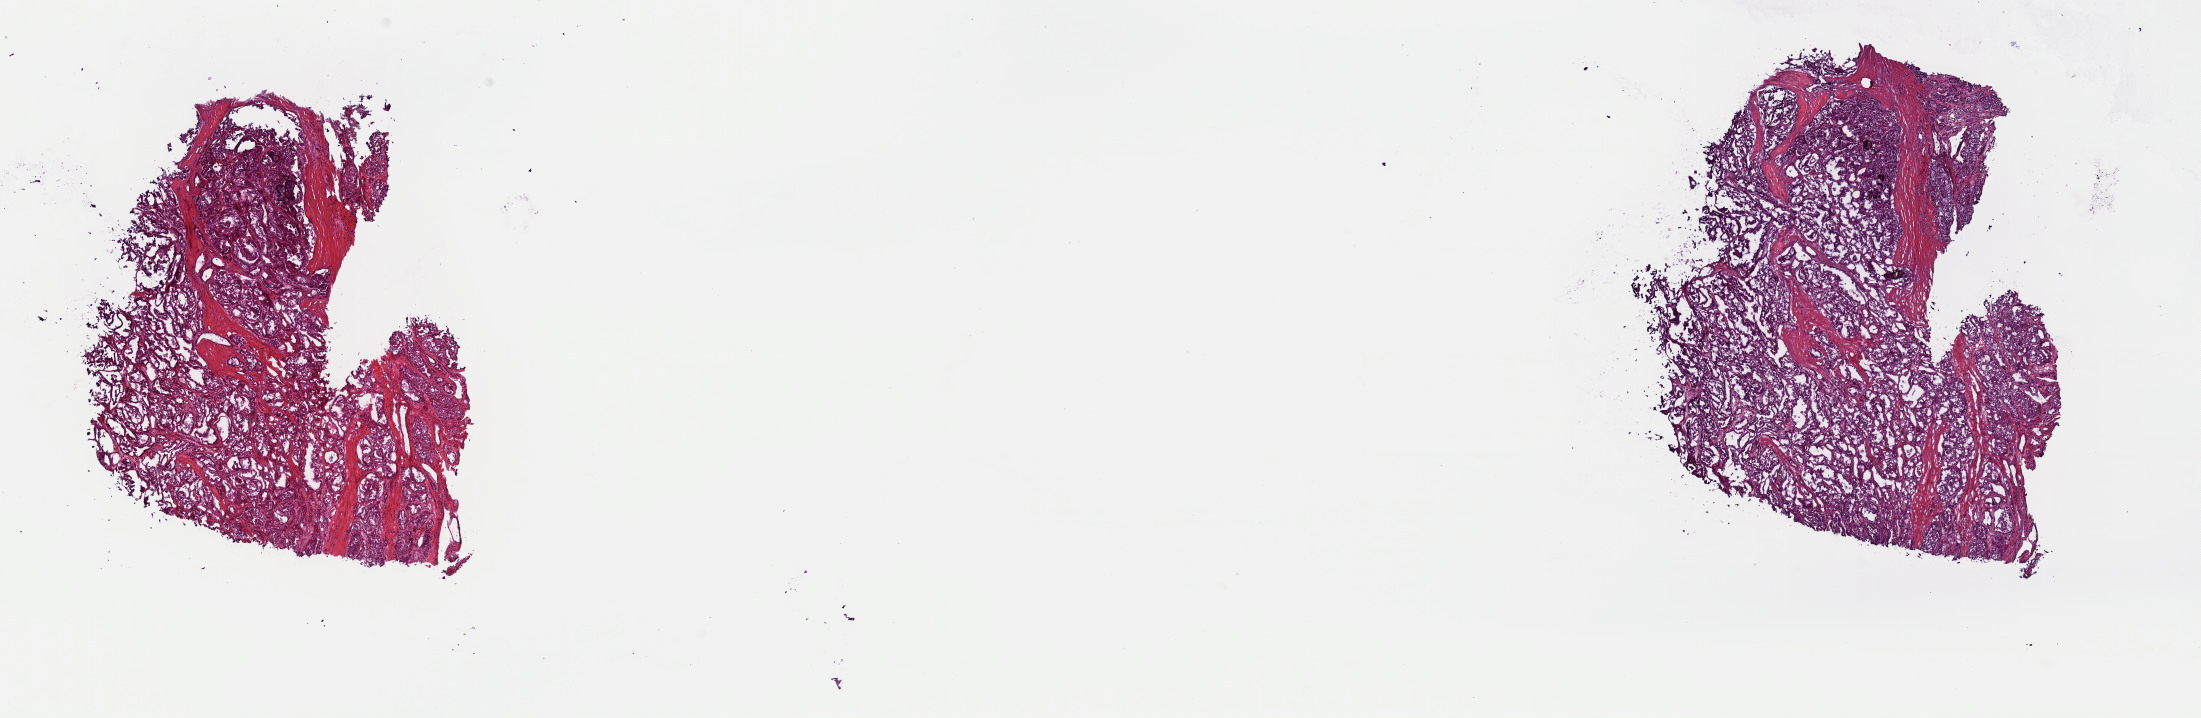
Digitized H&E-stained tissue section (whole slide) — a low-resolution overview of the entire scanned area, about 17.4 x 5.7 mm (from a 40x scan), frozen section, primary tumour sample from the thyroid. Male, age 63 years at initial diagnosis. Composition of this section per pathologist review: tumour cells 100%, tumour nuclei 88%, normal cells 0%, stromal cells 0%, necrosis 0%. Infiltration values recorded for this section: lymphocyte infiltration 0%, monocyte infiltration 0%, neutrophil infiltration 0%.
• histologic diagnosis: Papillary adenocarcinoma, NOS (thyroid gland)
• AJCC pathologic stage: IVA
• lymph nodes positive (case pathology): 6 of 25 examined